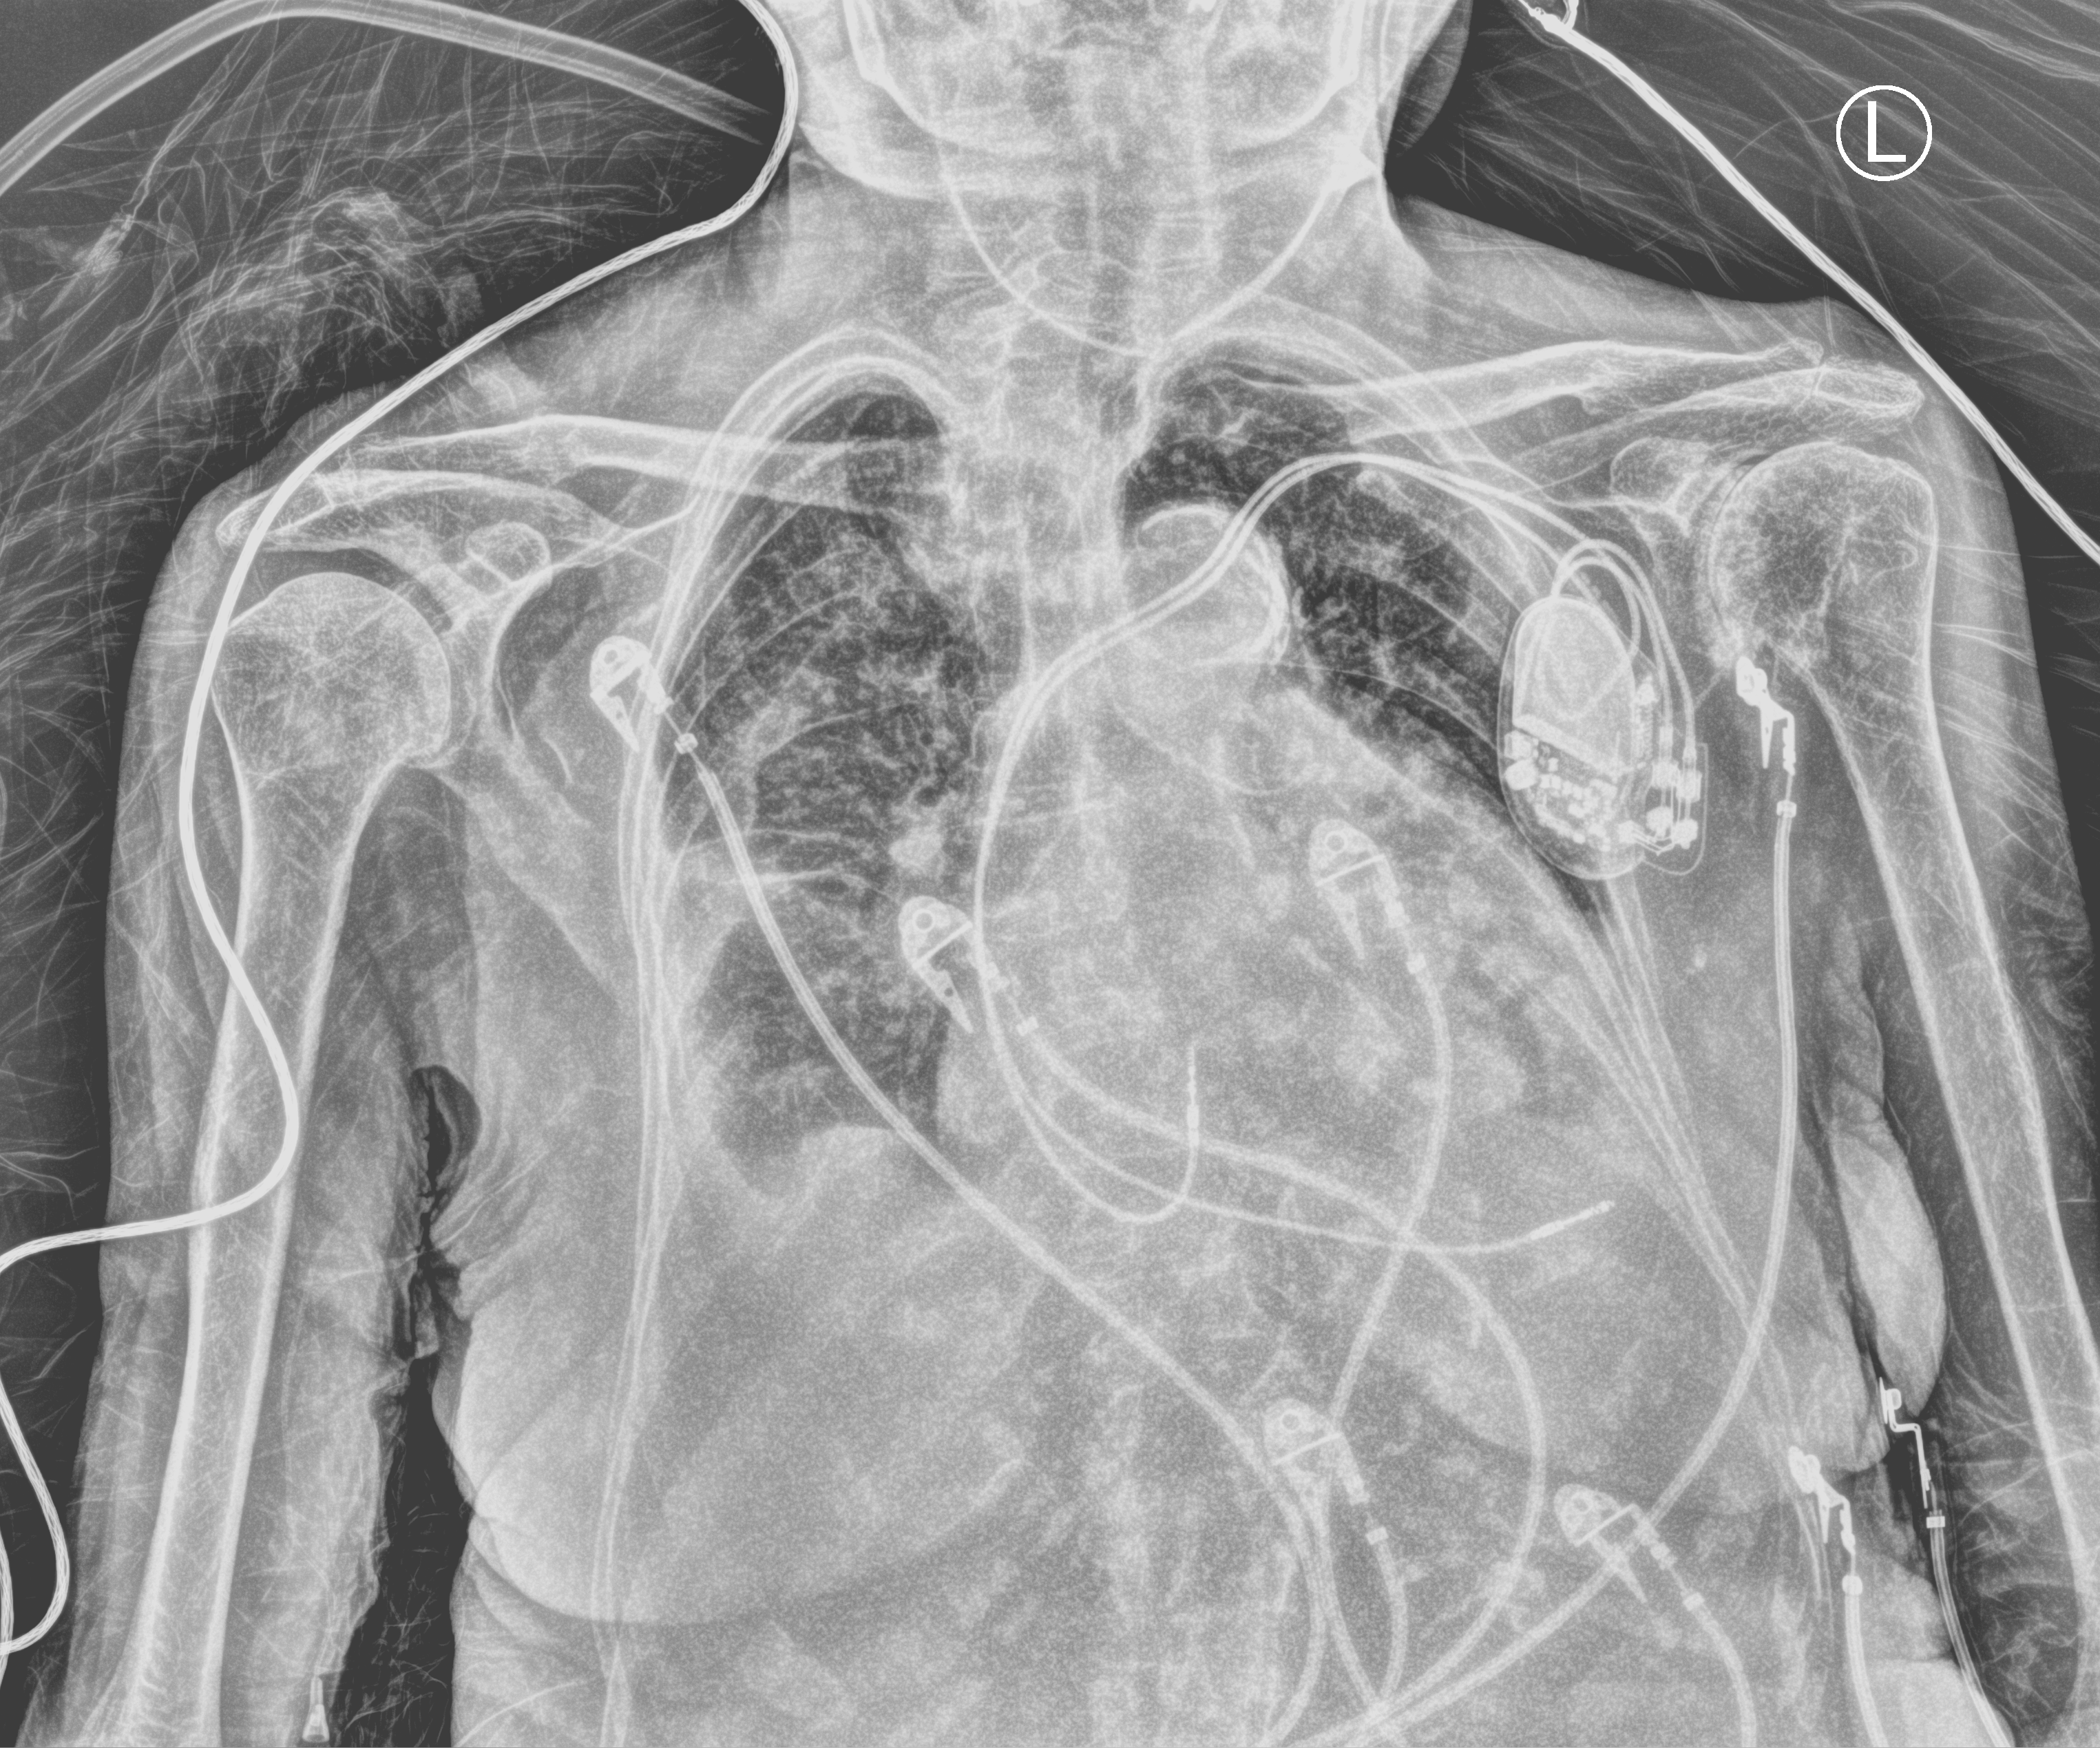
Chest X-ray (portable), anteroposterior (AP) projection. Female patient hospitalised with COVID-19, age 75–90 years.
Admission-level facts for this patient (not findings on this image; timing relative to this image not recorded): length of hospital stay: 5 days; chronic kidney disease (admission record): no.